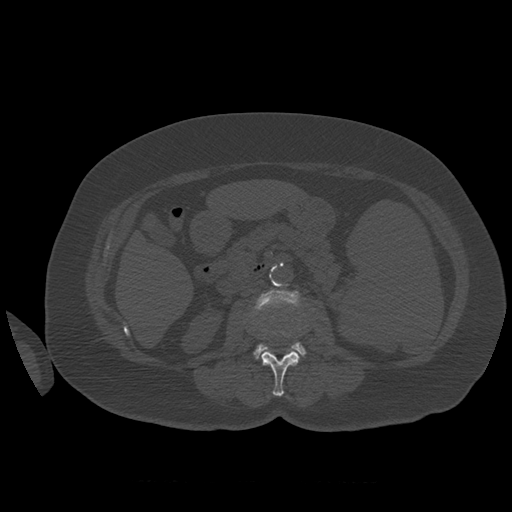
CT including the spine, one axial slice. Slice 244 of 399 in the series (ordered by position). Reconstruction kernel STANDARD. Bone window (W 1800 / L 400 HU). 512 × 512 image matrix, field of view 404 × 404 mm. Patient age 81 years. Case-level facts recorded for this patient, not image findings: primary cancer: renal; vertebrae with lytic lesions (as recorded): L1.
Structures marked on this image (semi-automatic segmentation, software-assisted and operator-edited):
- L2 vertebra: bounding box [x1, y1, x2, y2] px = [262, 330, 300, 397]
- L3 vertebra: [254, 290, 306, 360]